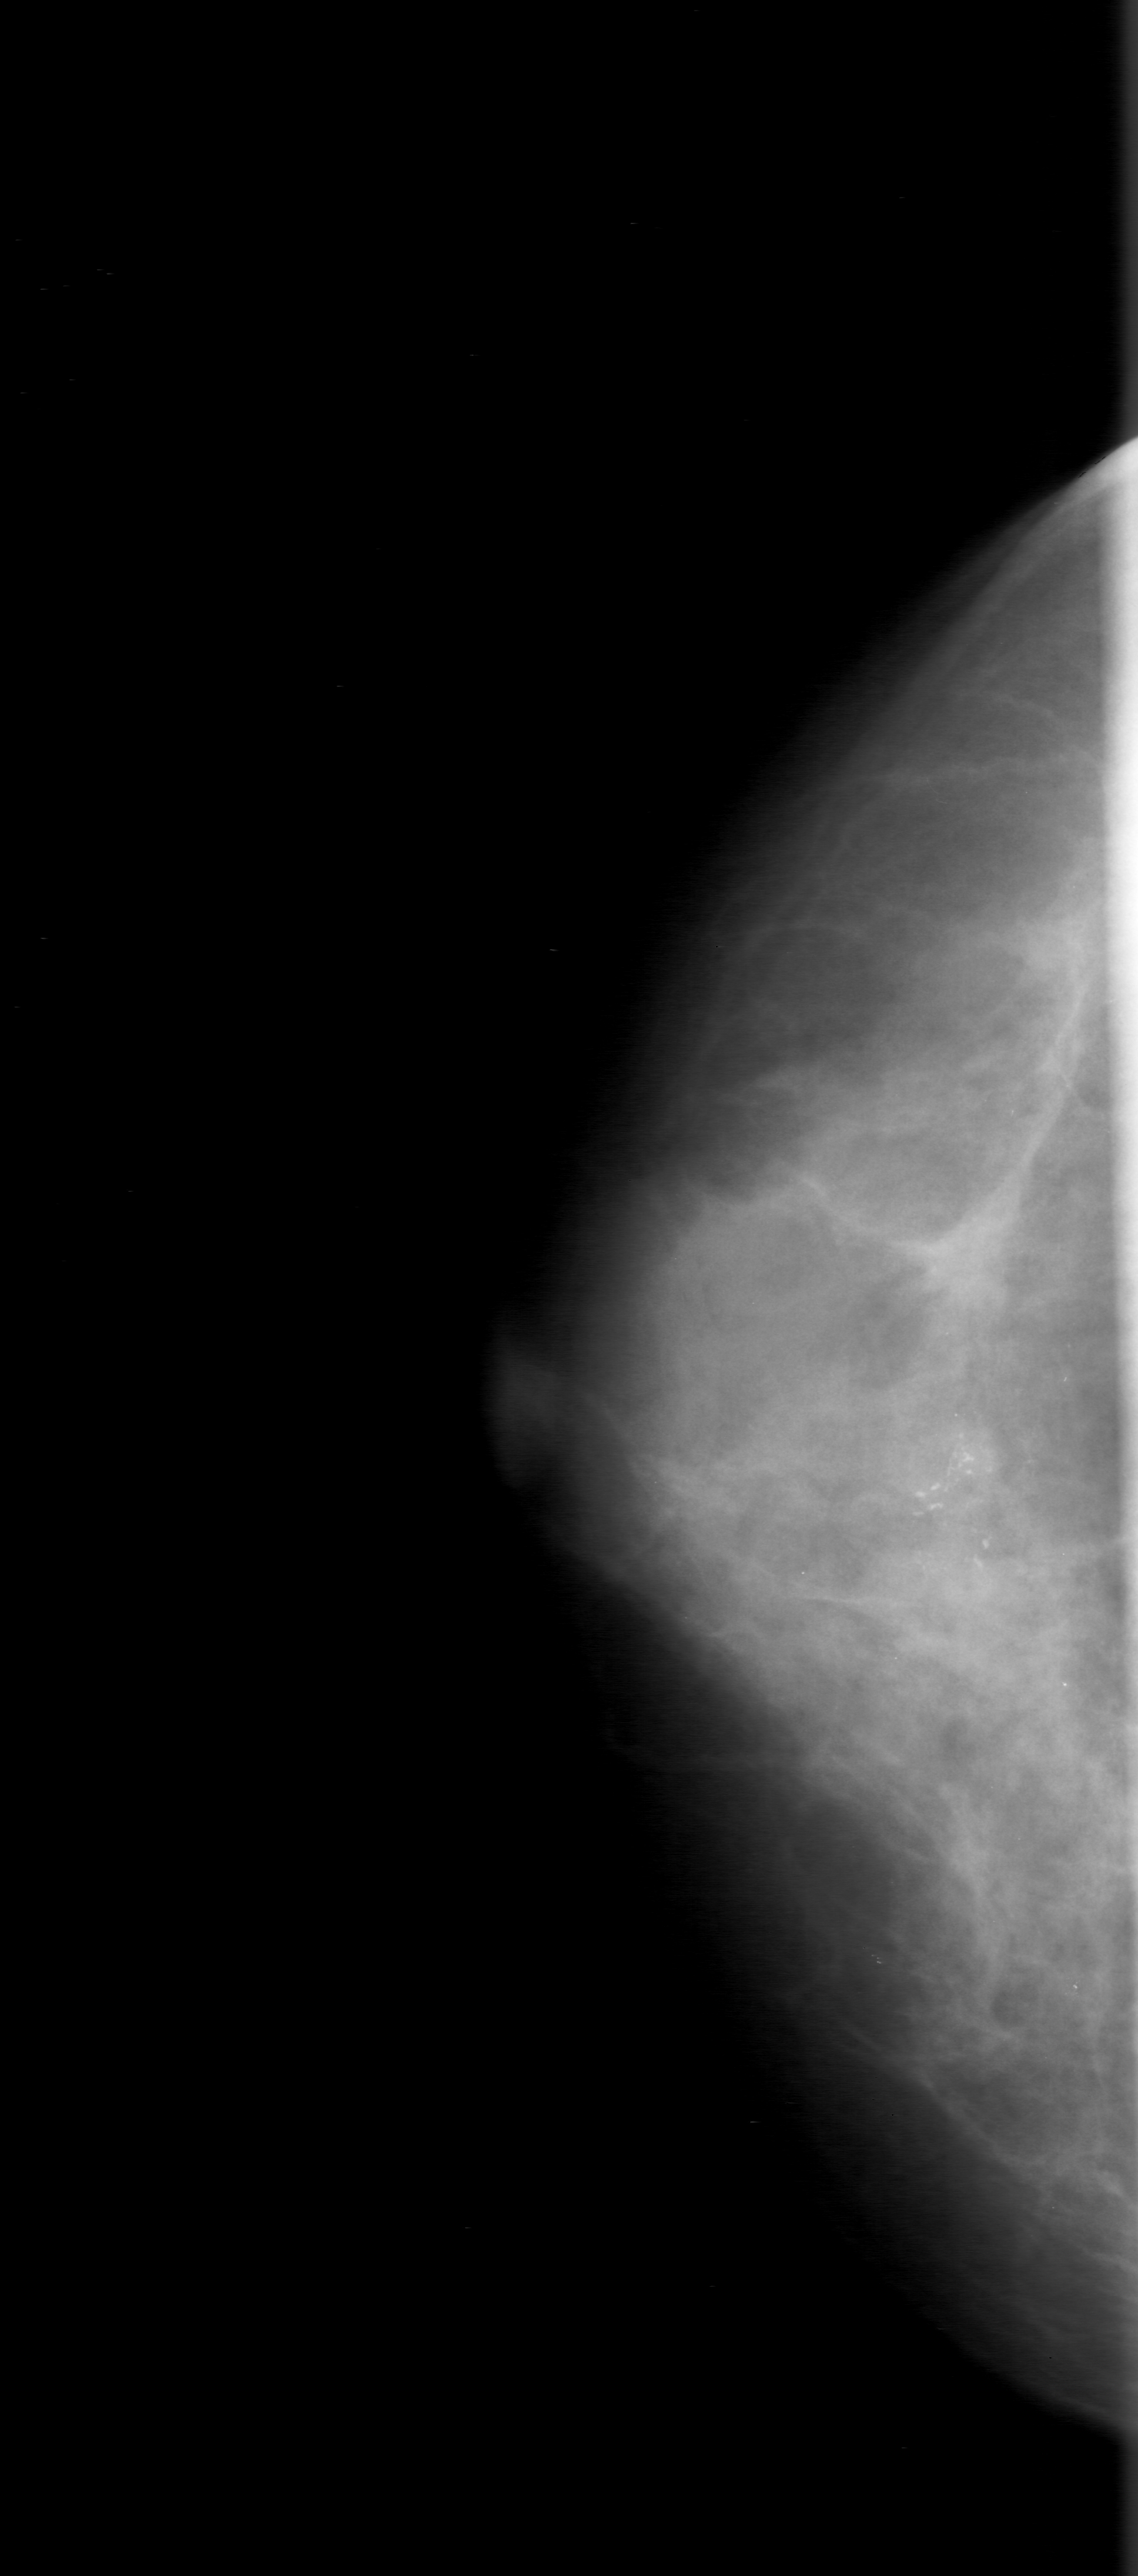
Mammogram (digitized film). Right breast. Craniocaudal (CC) view. Breast composition: heterogeneously dense (BI-RADS density category 3 of 4). 1138 × 2576 image matrix.
Marked abnormalities (boxes around the expert regions of interest):
- calcifications, morphology fine linear branching, distribution clustered; BI-RADS assessment category 3; pathology result (as recorded, not read from the image): malignant: bounding box [x1, y1, x2, y2] px = [808, 1357, 1130, 1690]